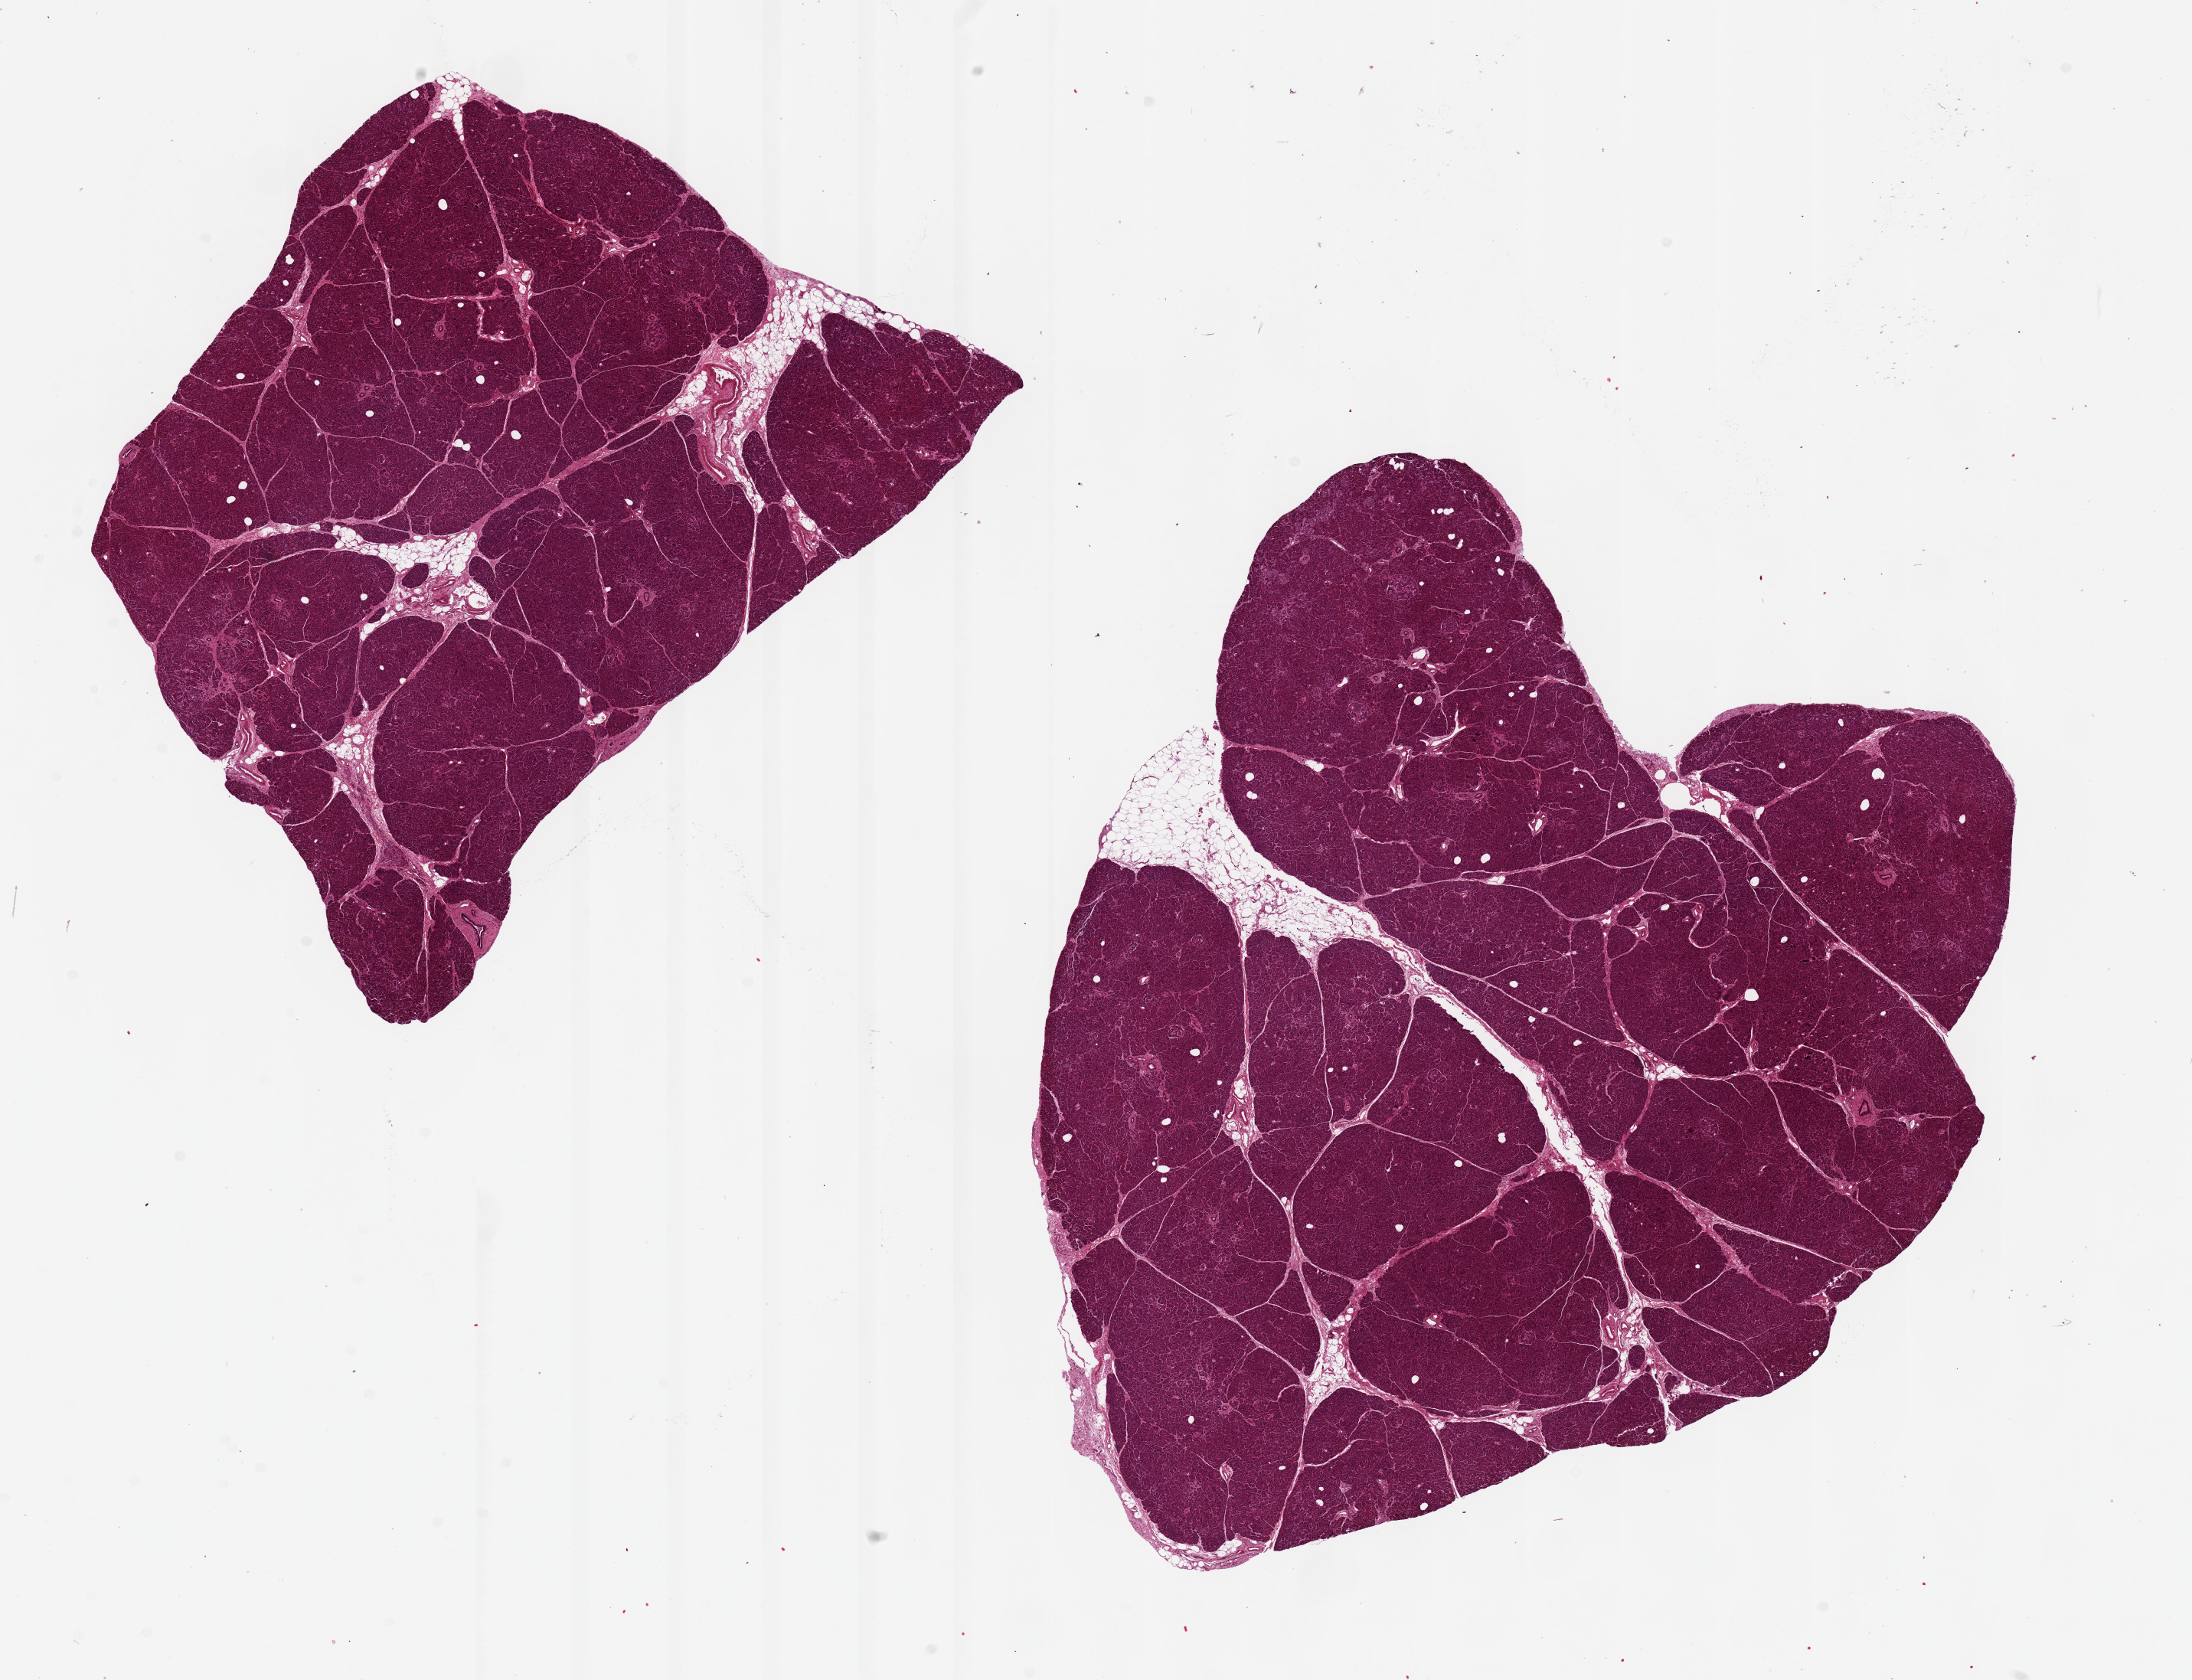
Whole-slide image, H&E stain, brightfield, low-resolution overview of the scanned area, about 22.6 x 17.4 mm (from a 20x scan), PAXgene-fixed, paraffin-embedded tissue, target tissue: pancreas, donor tissue sample. Donor sex: male.
Reviewer comment on this tissue sample: 2 ~8.5x7.5mm aliquots. Exceptionally well-preserved; Islets appear reduced in number.